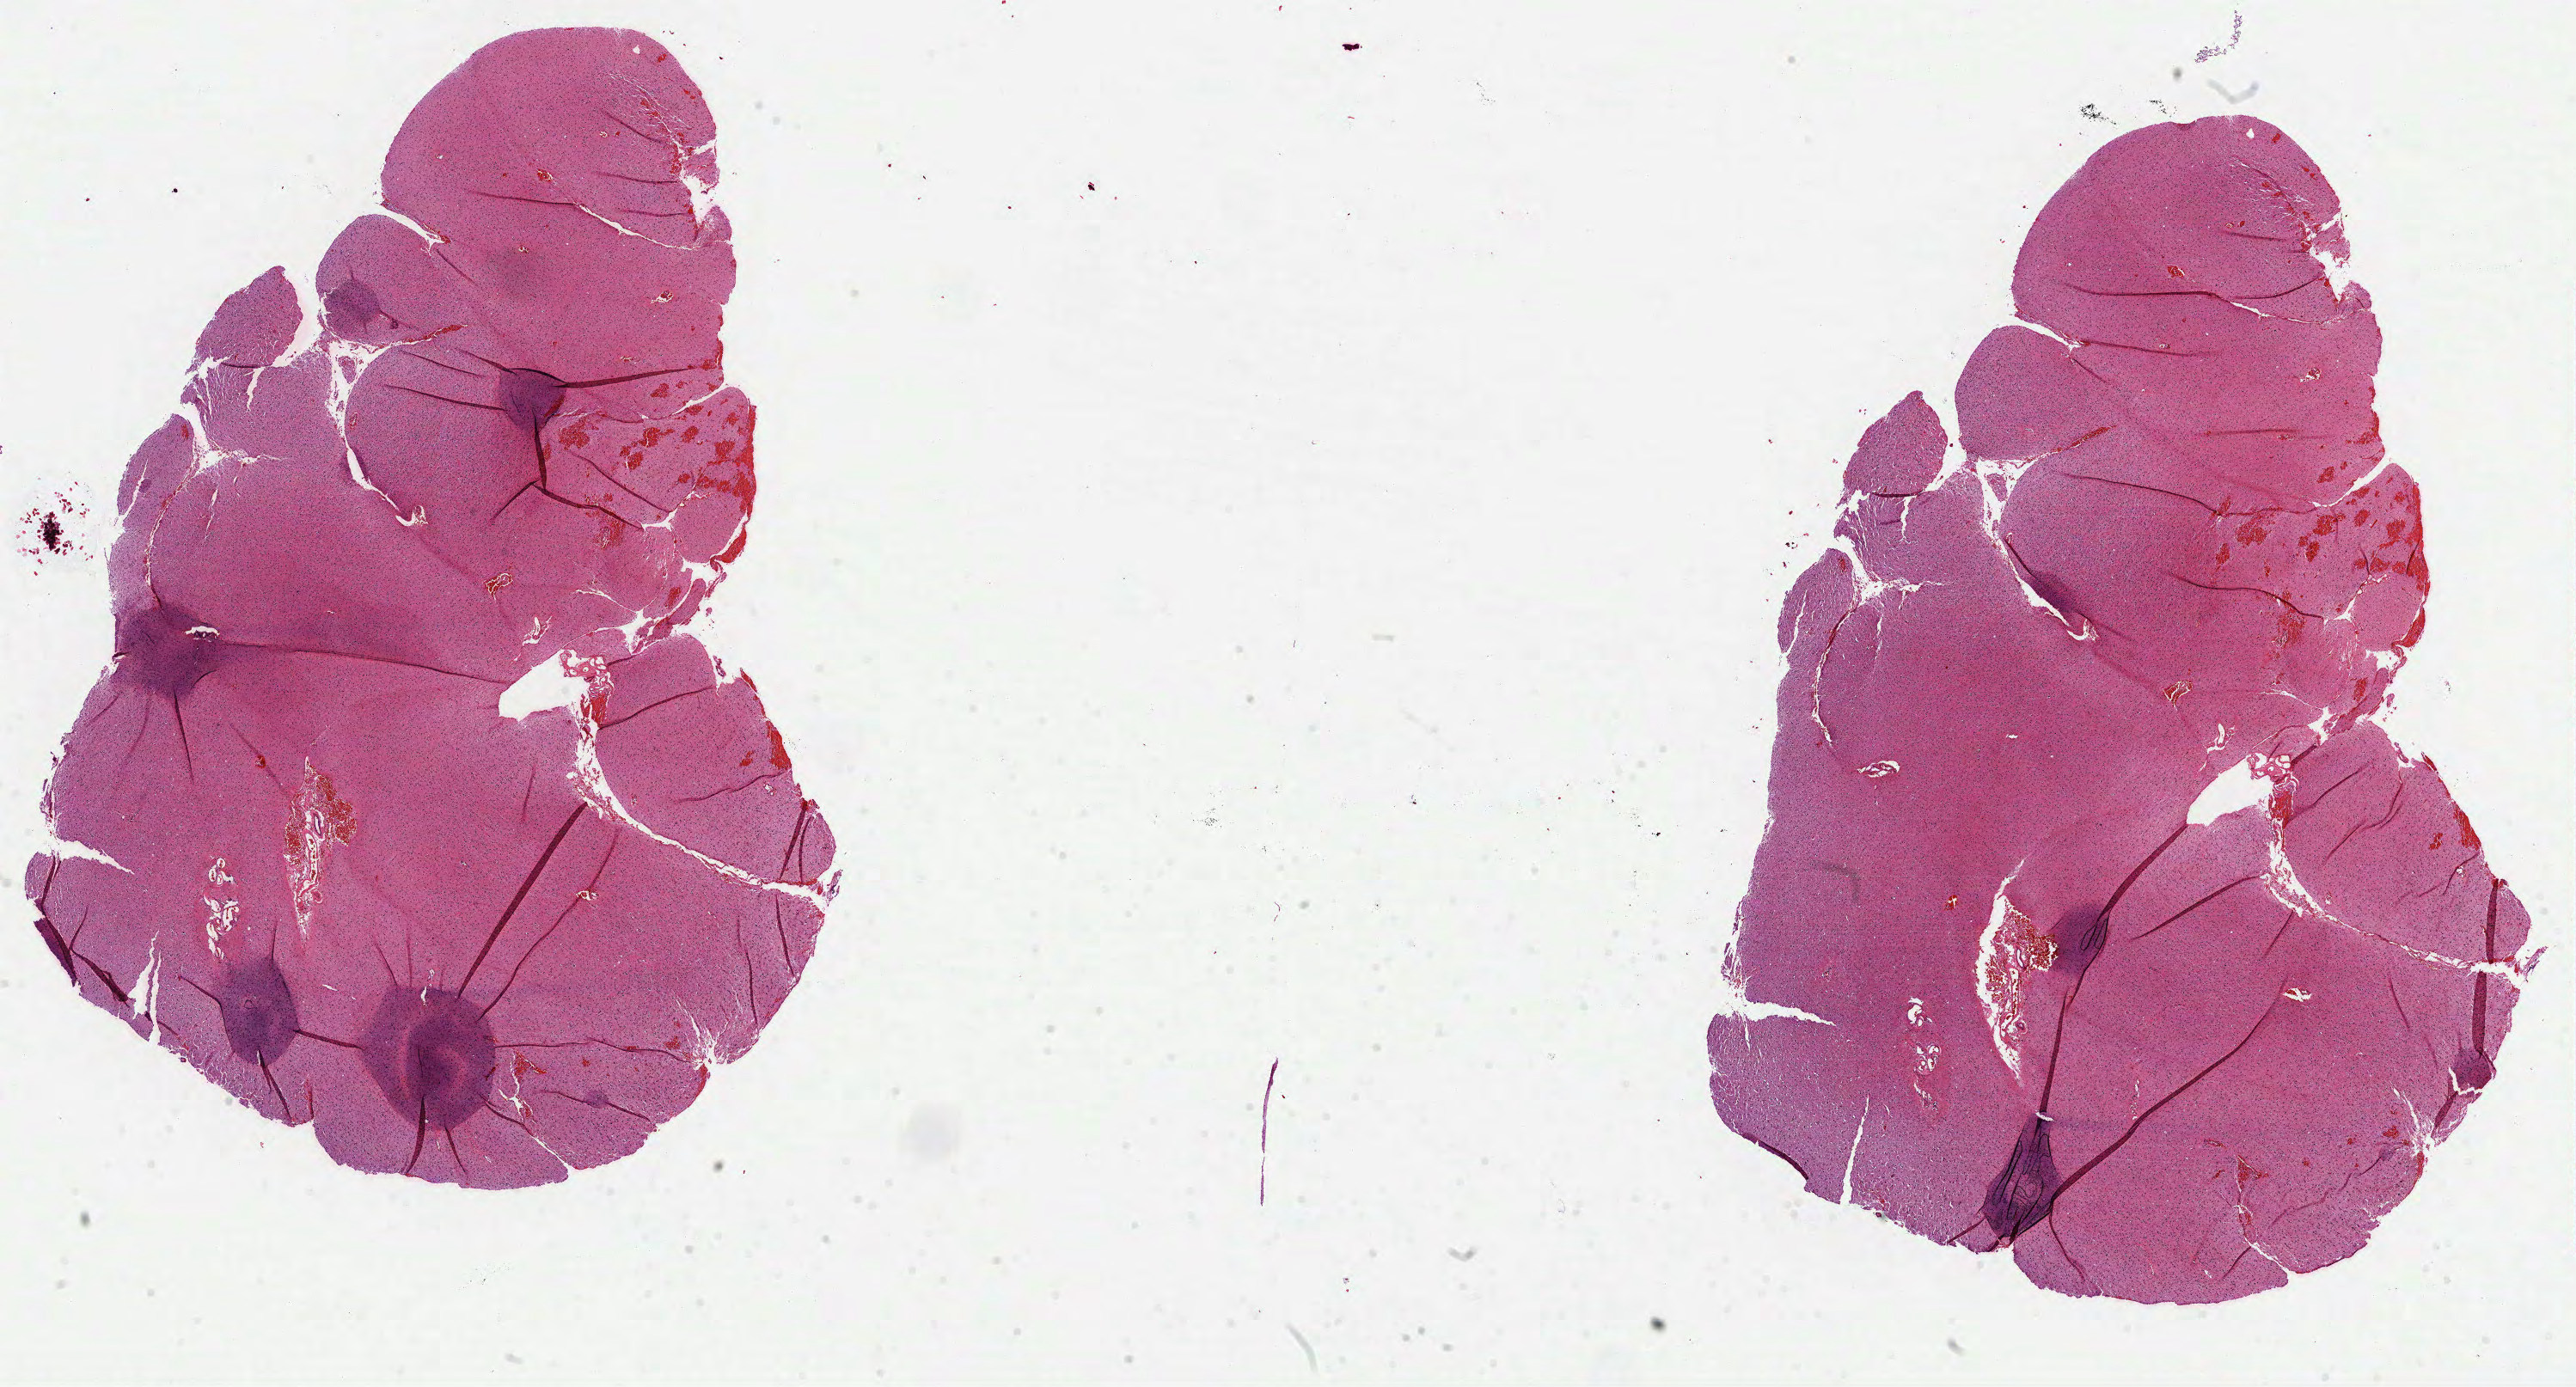
Whole-slide histology image, Hematoxylin and eosin (H&E) stained, whole scanned area (about 24.2 x 13.0 mm, acquisition: 40x scan) shown as a low-resolution overview; formalin-fixed paraffin-embedded (FFPE) diagnostic section; sample: primary tumour, brain. Patient: female, age at initial diagnosis 51 years. Histologic grade: G3 (poorly differentiated).
- pathologic diagnosis: Astrocytoma, anaplastic